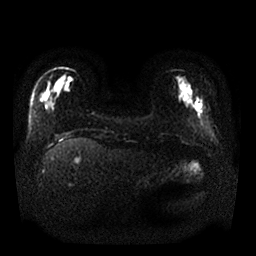
Breast MRI, one axial slice; position 6 of 25 along the scan axis; diffusion-weighted series; image 2 of 4 stored at this slice position (different b-values; order by instance number); 1.5 T; 256 × 256 image matrix, field of view 340 × 340 mm. Female patient.
Structures marked on this image (outlined manually by an expert reader):
- tumour on diffusion-weighted imaging: box from (x=196, y=97) to (x=204, y=118) px